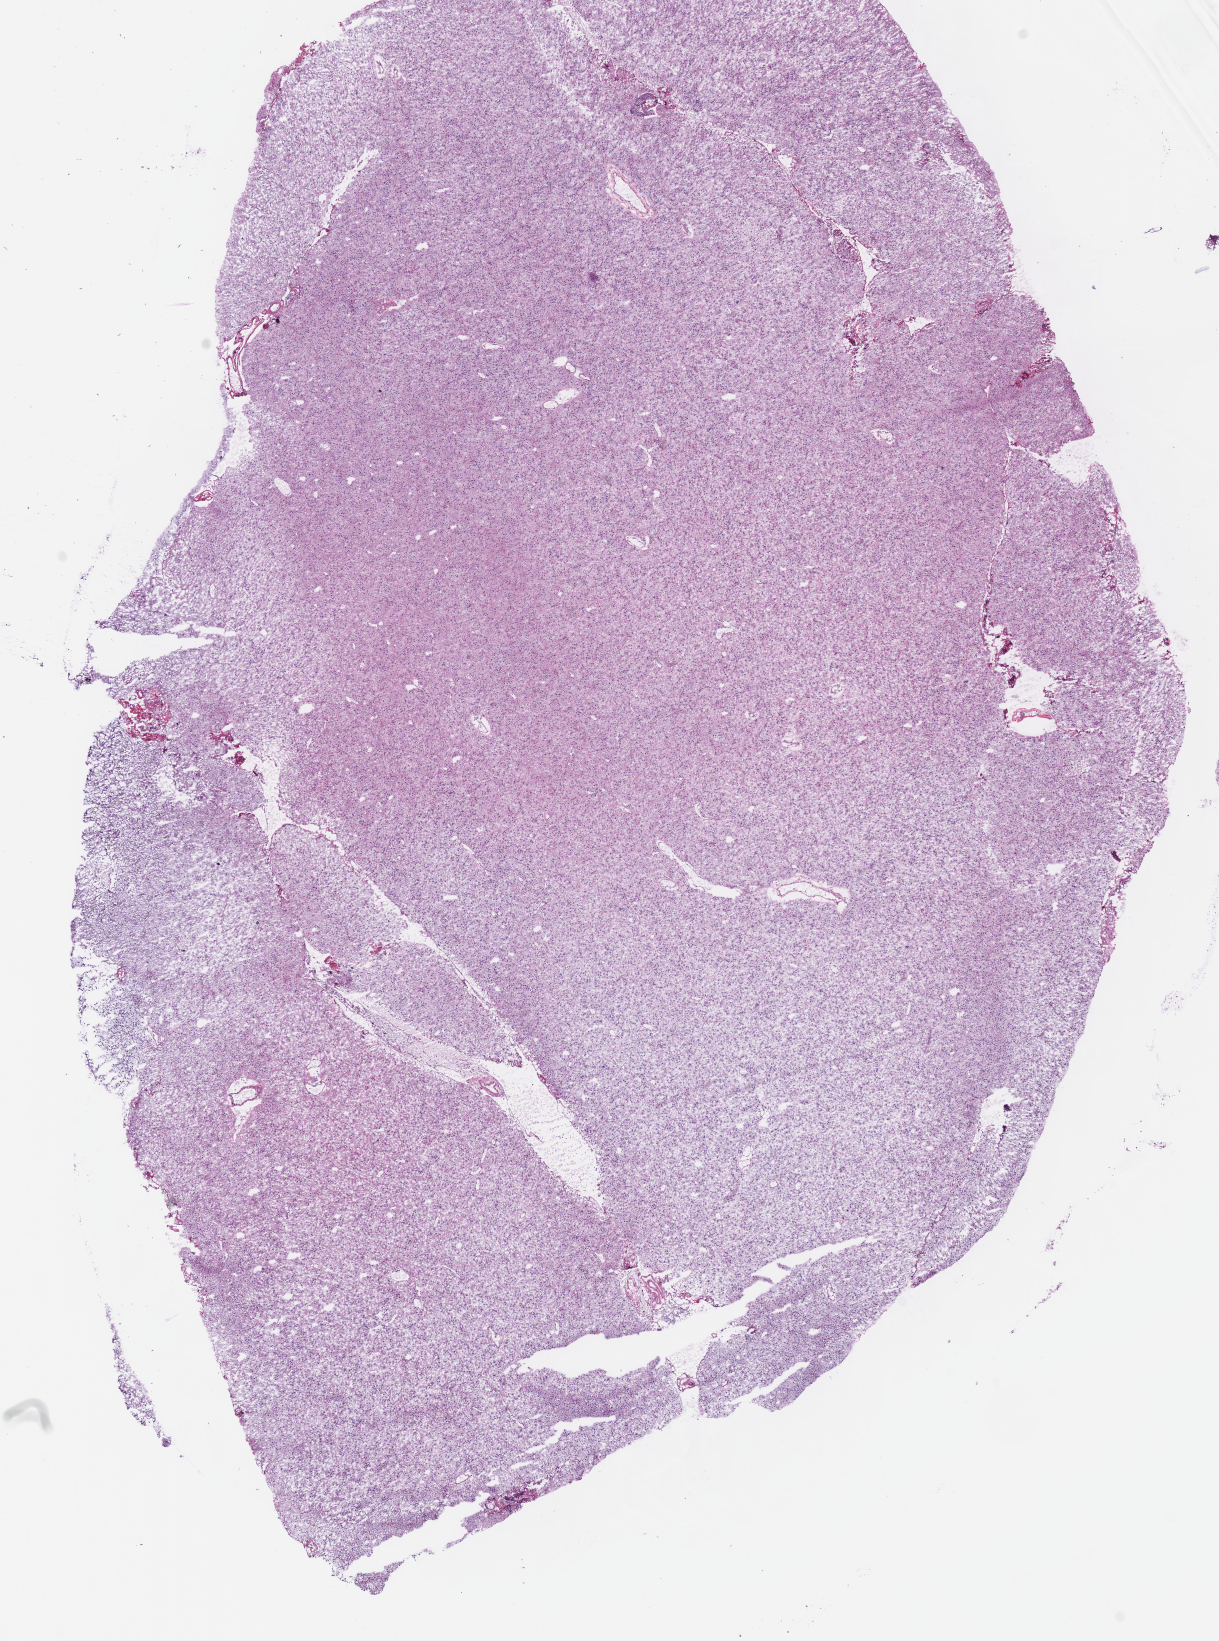
Whole-slide histology image, H&E — whole scanned area (about 9.6 x 12.9 mm) shown as a low-resolution overview, frozen section from the bottom of the tissue portion, sample: primary tumour, brain. Male patient; age at initial diagnosis 30 years. Histologic grade: G3 (poorly differentiated). Slide review estimates, as recorded: tumour cells 100%, tumour nuclei 80%, normal cells 0%, stromal cells 0%, necrosis 0%.
Pathologic diagnosis: Oligodendroglioma, anaplastic (cerebrum). Laterality: right.